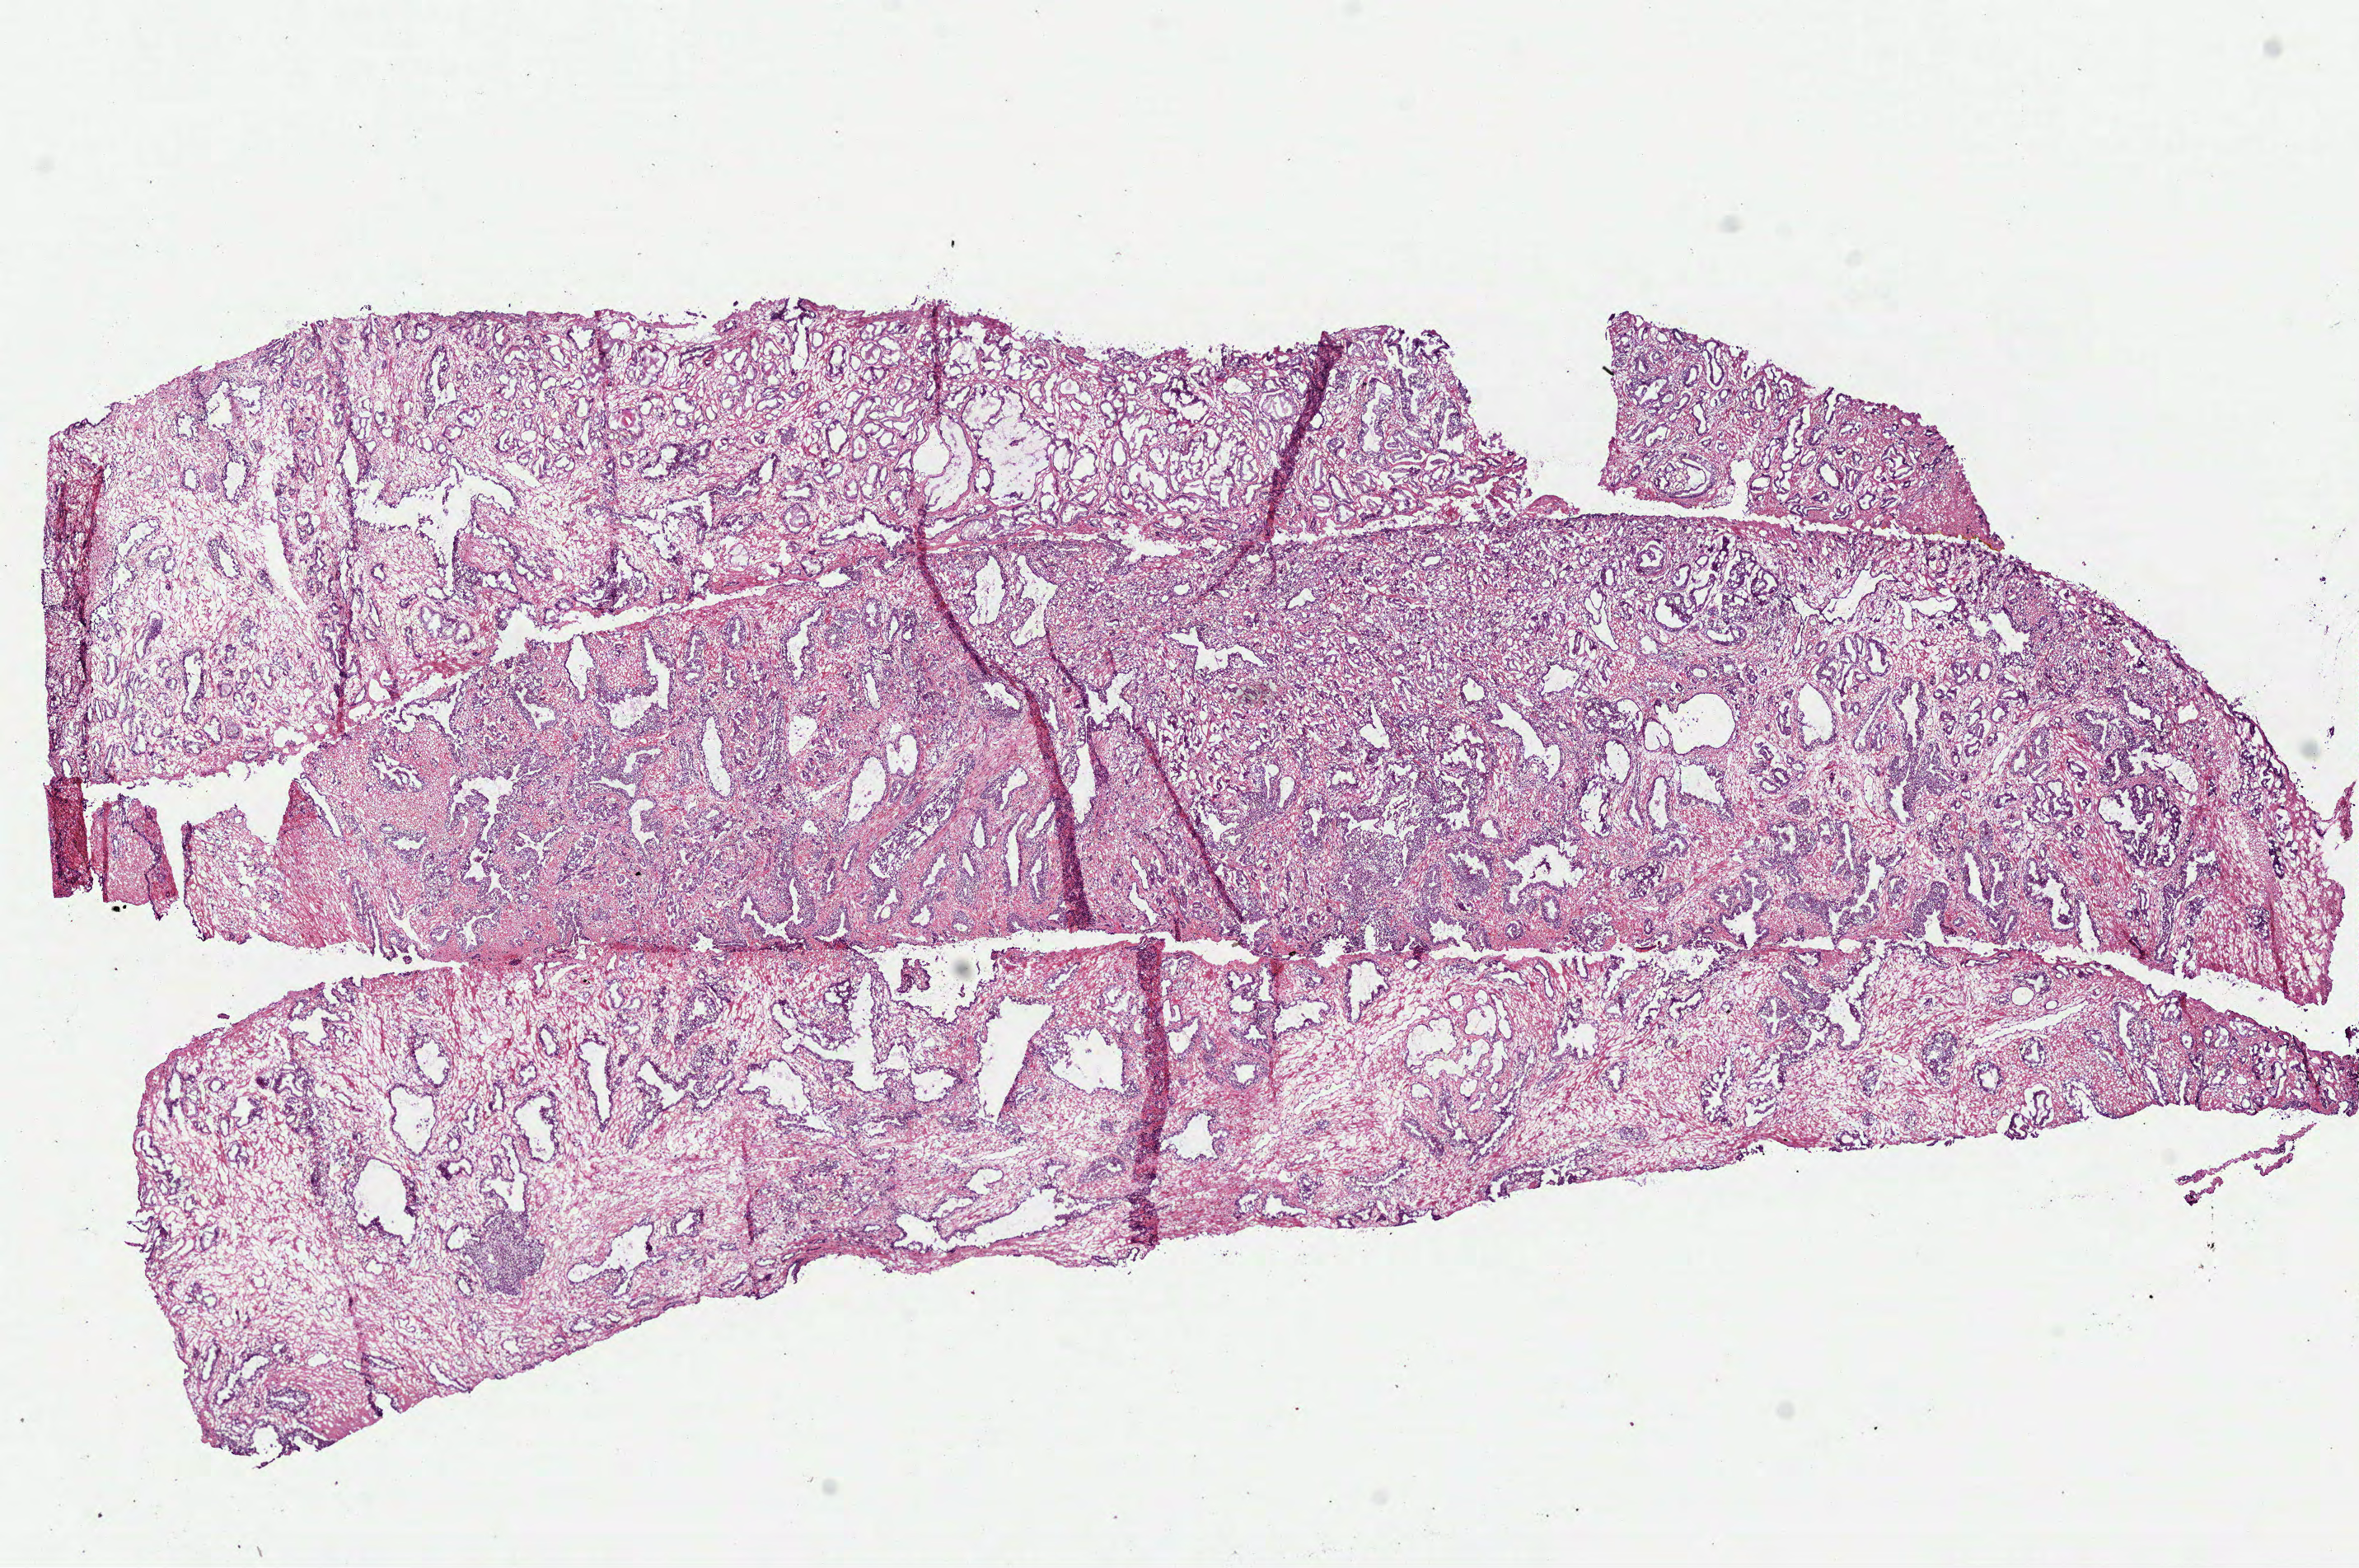
Whole-slide histology image, Hematoxylin and eosin (H&E) stained — whole scanned area (about 11.5 x 7.7 mm, slide scanned at 40x) shown as a low-resolution overview, frozen section, prostate, primary tumour sample. Male, age 60 years at initial diagnosis. Gleason score: 9 (4+5). Slide review estimates, as recorded: tumour cells 60%, tumour nuclei 60%, normal cells 20%, stromal cells 20%, necrosis 0%. Inflammatory infiltration, as recorded: lymphocyte infiltration 1%, monocyte infiltration 0%, neutrophil infiltration 0%.
Histologic diagnosis: Acinar cell carcinoma (prostate gland).